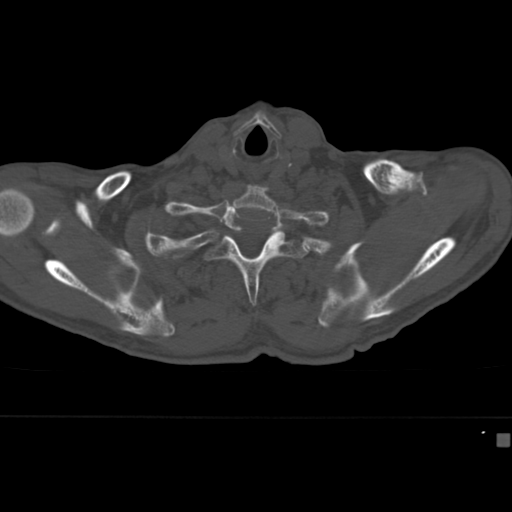
CT including the spine, one axial slice. Slice 347 of 430 in the series (ordered by position). Reconstruction kernel Br40s. 120 kVp. Bone window (W 1800 / L 400 HU). 1.5 mm slice thickness. 512 × 512 image matrix. Patient: male, 64 years. From the clinical record (not read from this slice): primary cancer: uterus; vertebrae with lytic lesions (as recorded): T1, T4, T5, T7, L5.
Outlined on this slice (semi-automatically segmented with operator editing):
- T2 vertebra: bounding box (x1, y1, x2, y2) in pixels: (203, 233, 309, 305)
- T3 vertebra: (204, 274, 209, 280)